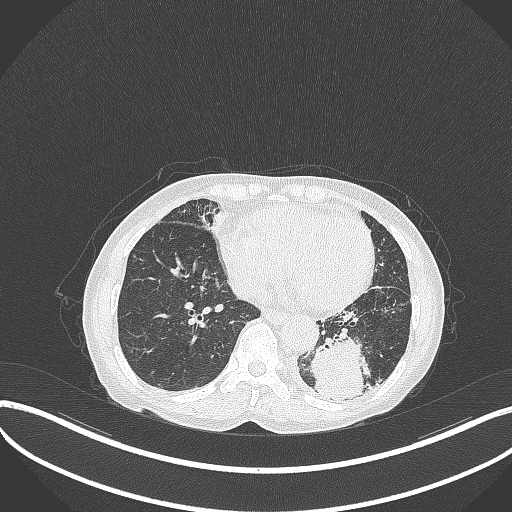
Chest CT, one axial slice; position 97 of 370 along the scan axis; reconstruction kernel B70f; lung window (W 1500 / L -600 HU); 512 × 512 image matrix, field of view 400 × 400 mm. Female patient, age 78 years. Case-level facts recorded for this patient, not image findings: clinical TNM (as recorded): T3 N0 M1.
Structures marked on this image (bounding box drawn by a radiologist):
- lung tumour (recorded histology: squamous cell carcinoma): box from (x=308, y=329) to (x=370, y=402) px